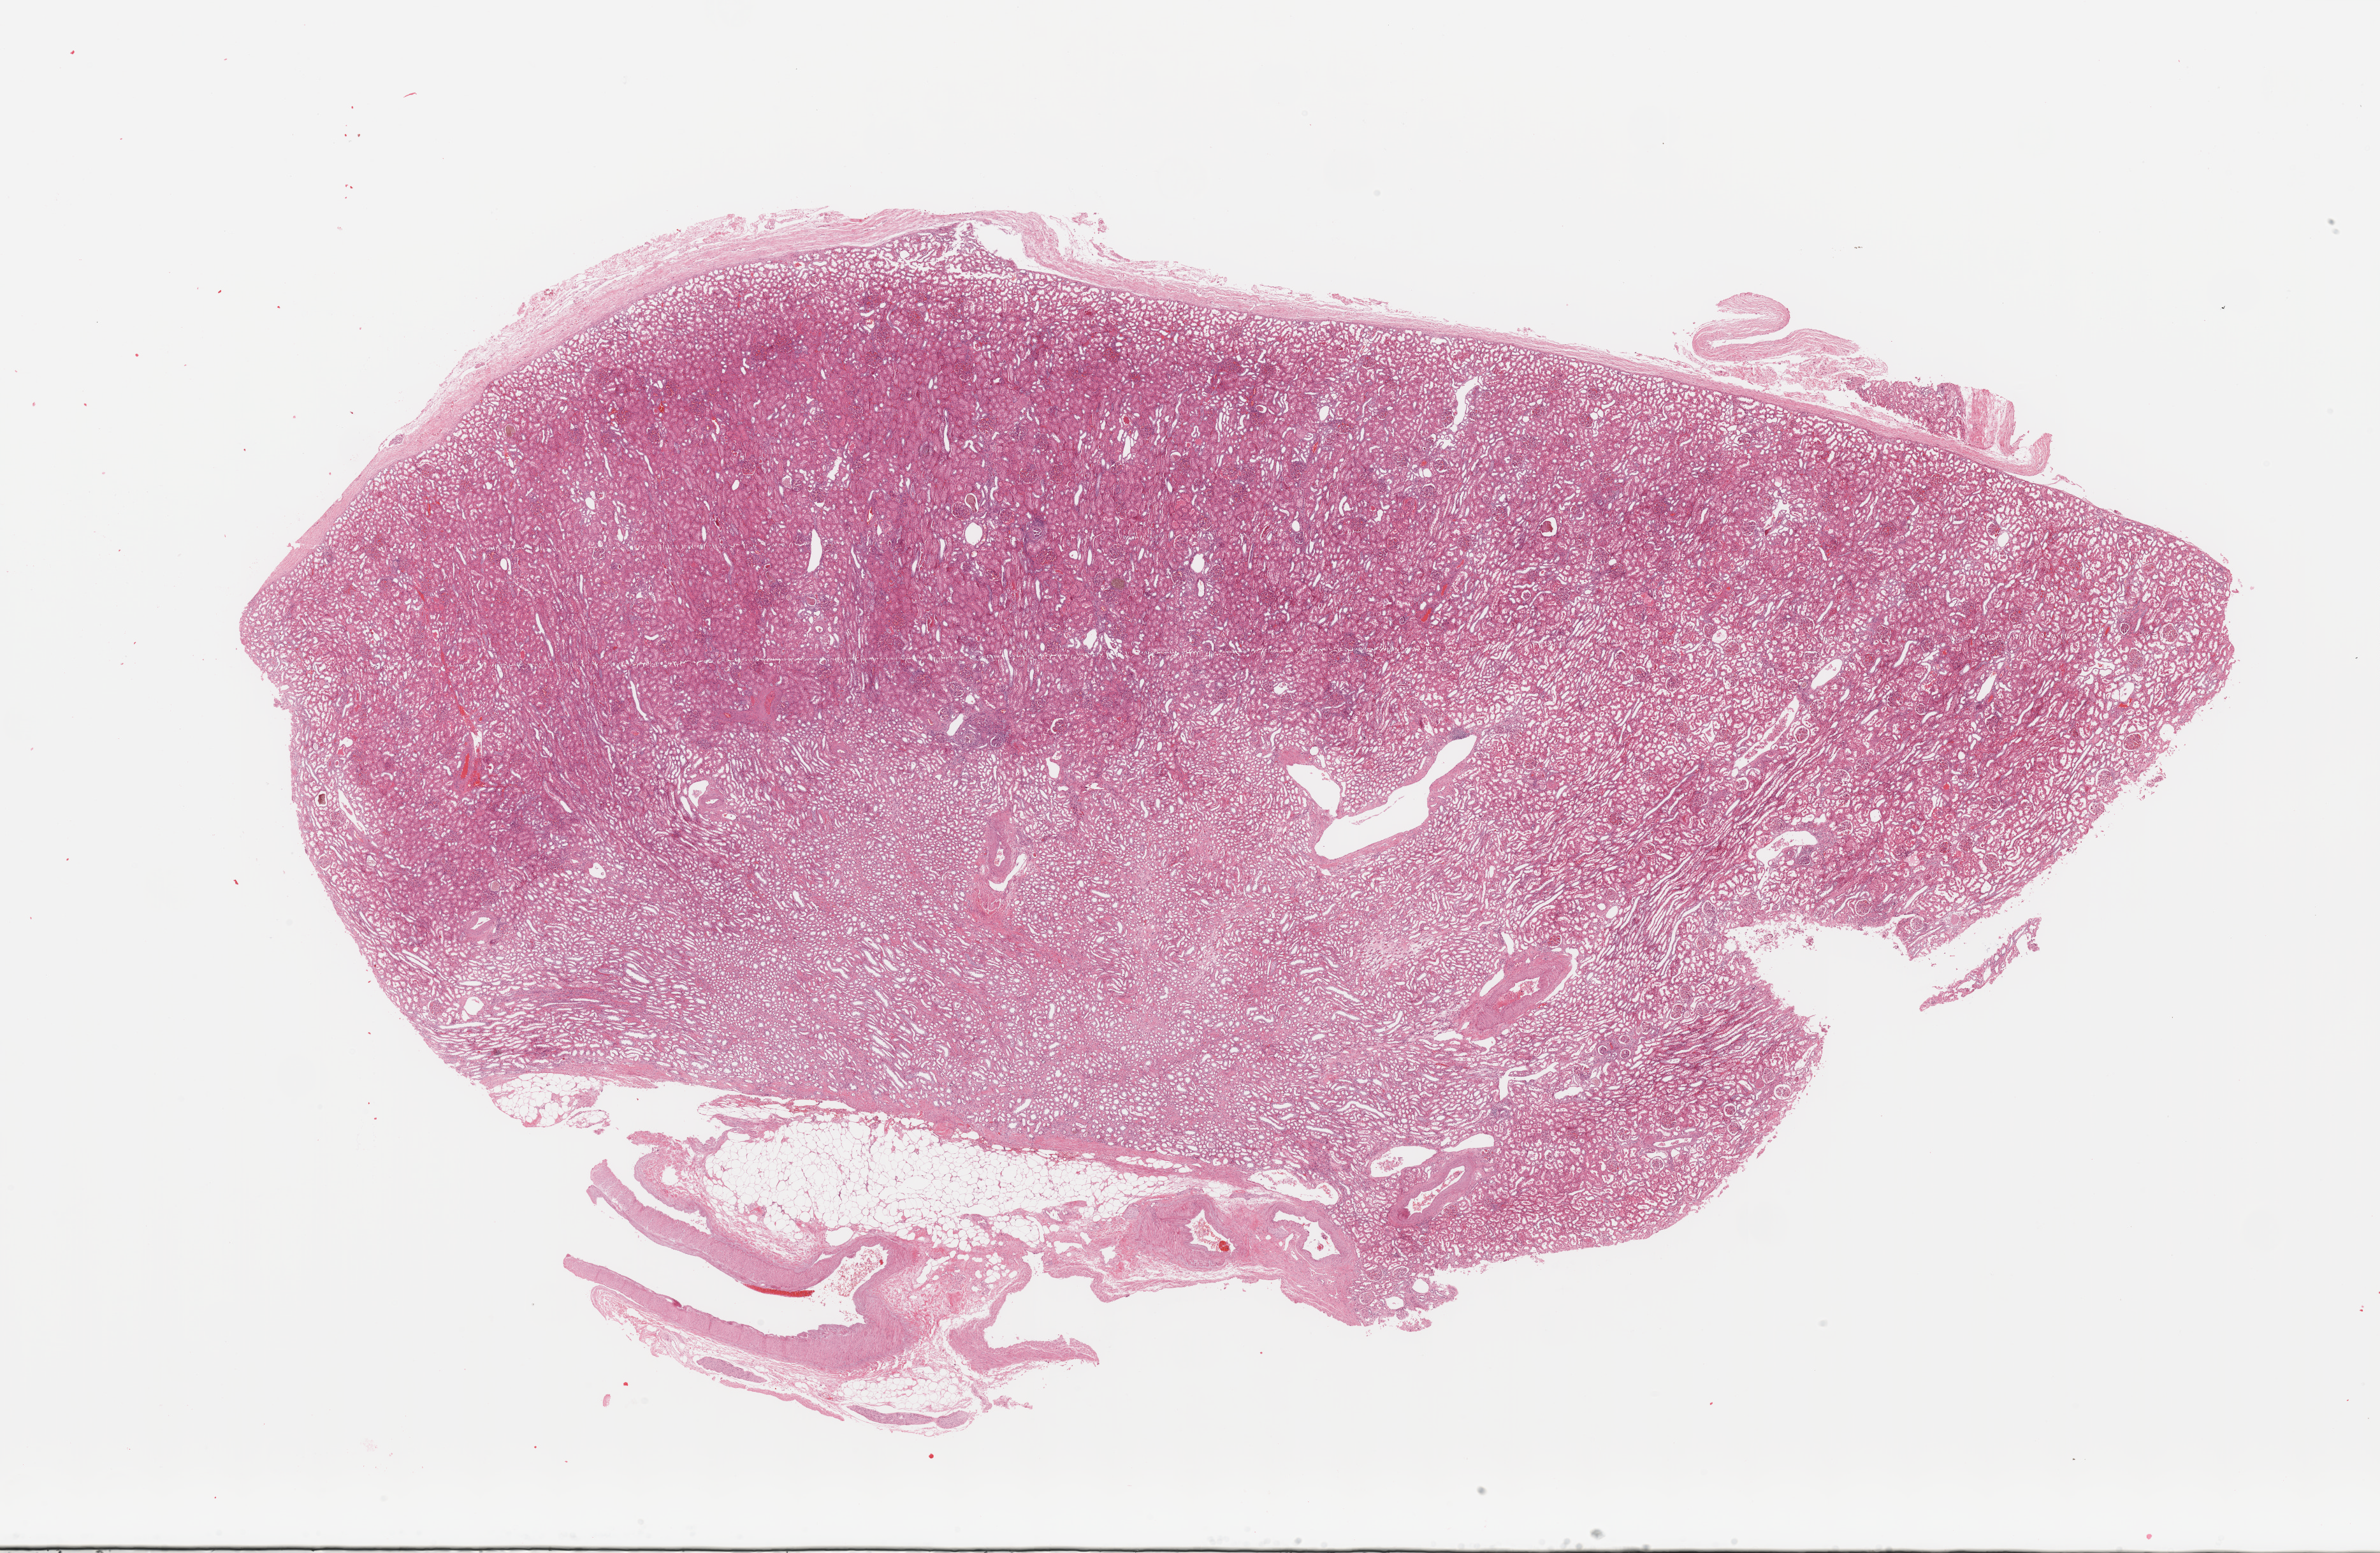
H&E whole-slide image, a low-resolution overview of the entire scanned area, about 29.5 x 19.3 mm, normal (non-tumour) tissue sample, sampled site: kidney. 54-year-old female patient.
This section: normal (non-tumour) tissue from the same patient. Patient diagnosis: Renal cell carcinoma, NOS.